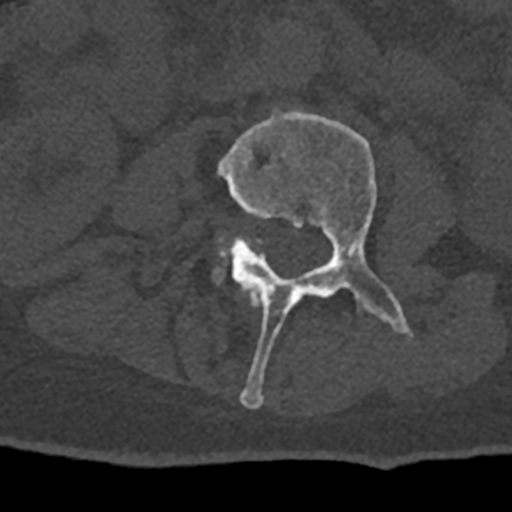
CT including the spine, one axial slice. Position 314 of 797 along the scan axis. Reconstruction kernel Br40s/3. 120 kVp. Bone window (W 1800 / L 400 HU). 0.5 mm slice thickness. 512 × 512 image matrix, field of view 160 × 160 mm. Male patient, age 74 years. Case-level facts recorded for this patient, not image findings: primary cancer: renal; vertebrae with lytic lesions (as recorded): T10, L1, L2, L3, L4, L5.
Outlined on this slice (semi-automatically segmented with operator editing):
- L2 vertebra: bounding box (x1, y1, x2, y2) in pixels: (250, 293, 262, 306)
- L3 vertebra: (218, 109, 414, 408)
- L4 vertebra: (215, 237, 250, 281)